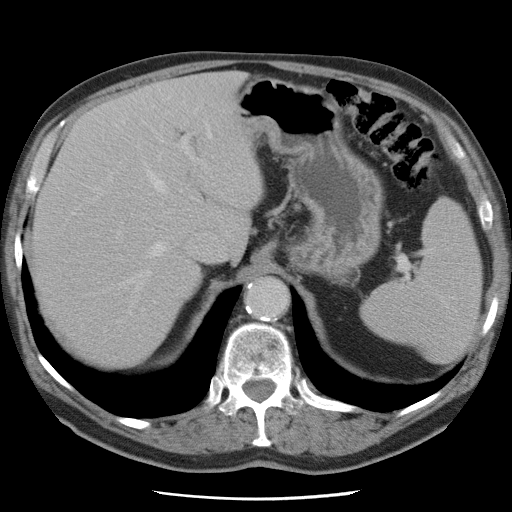
Contrast-enhanced abdominal CT, one axial slice; position 55 of 78 along the scan axis; intravenous contrast given; soft-tissue window (W 400 / L 40 HU); 5 mm slice thickness; 512 × 512 image matrix. Male patient, age 75 years. From the clinical record (not read from this slice): diagnosis: colorectal cancer liver metastases, imaged before liver resection; multiple liver metastases: yes; largest metastasis: 2.4 cm; disease in both lobes: yes.
Outlined on this slice (outlined manually by an expert reader):
- hepatic veins: bounding box <92,125,211,288> (left, top, right, bottom; pixels)
- liver: <35,74,261,362>
- planned liver remnant (the part of the liver to remain after resection): <35,129,199,362>
- portal vein (with intrahepatic branches): <108,136,197,240>